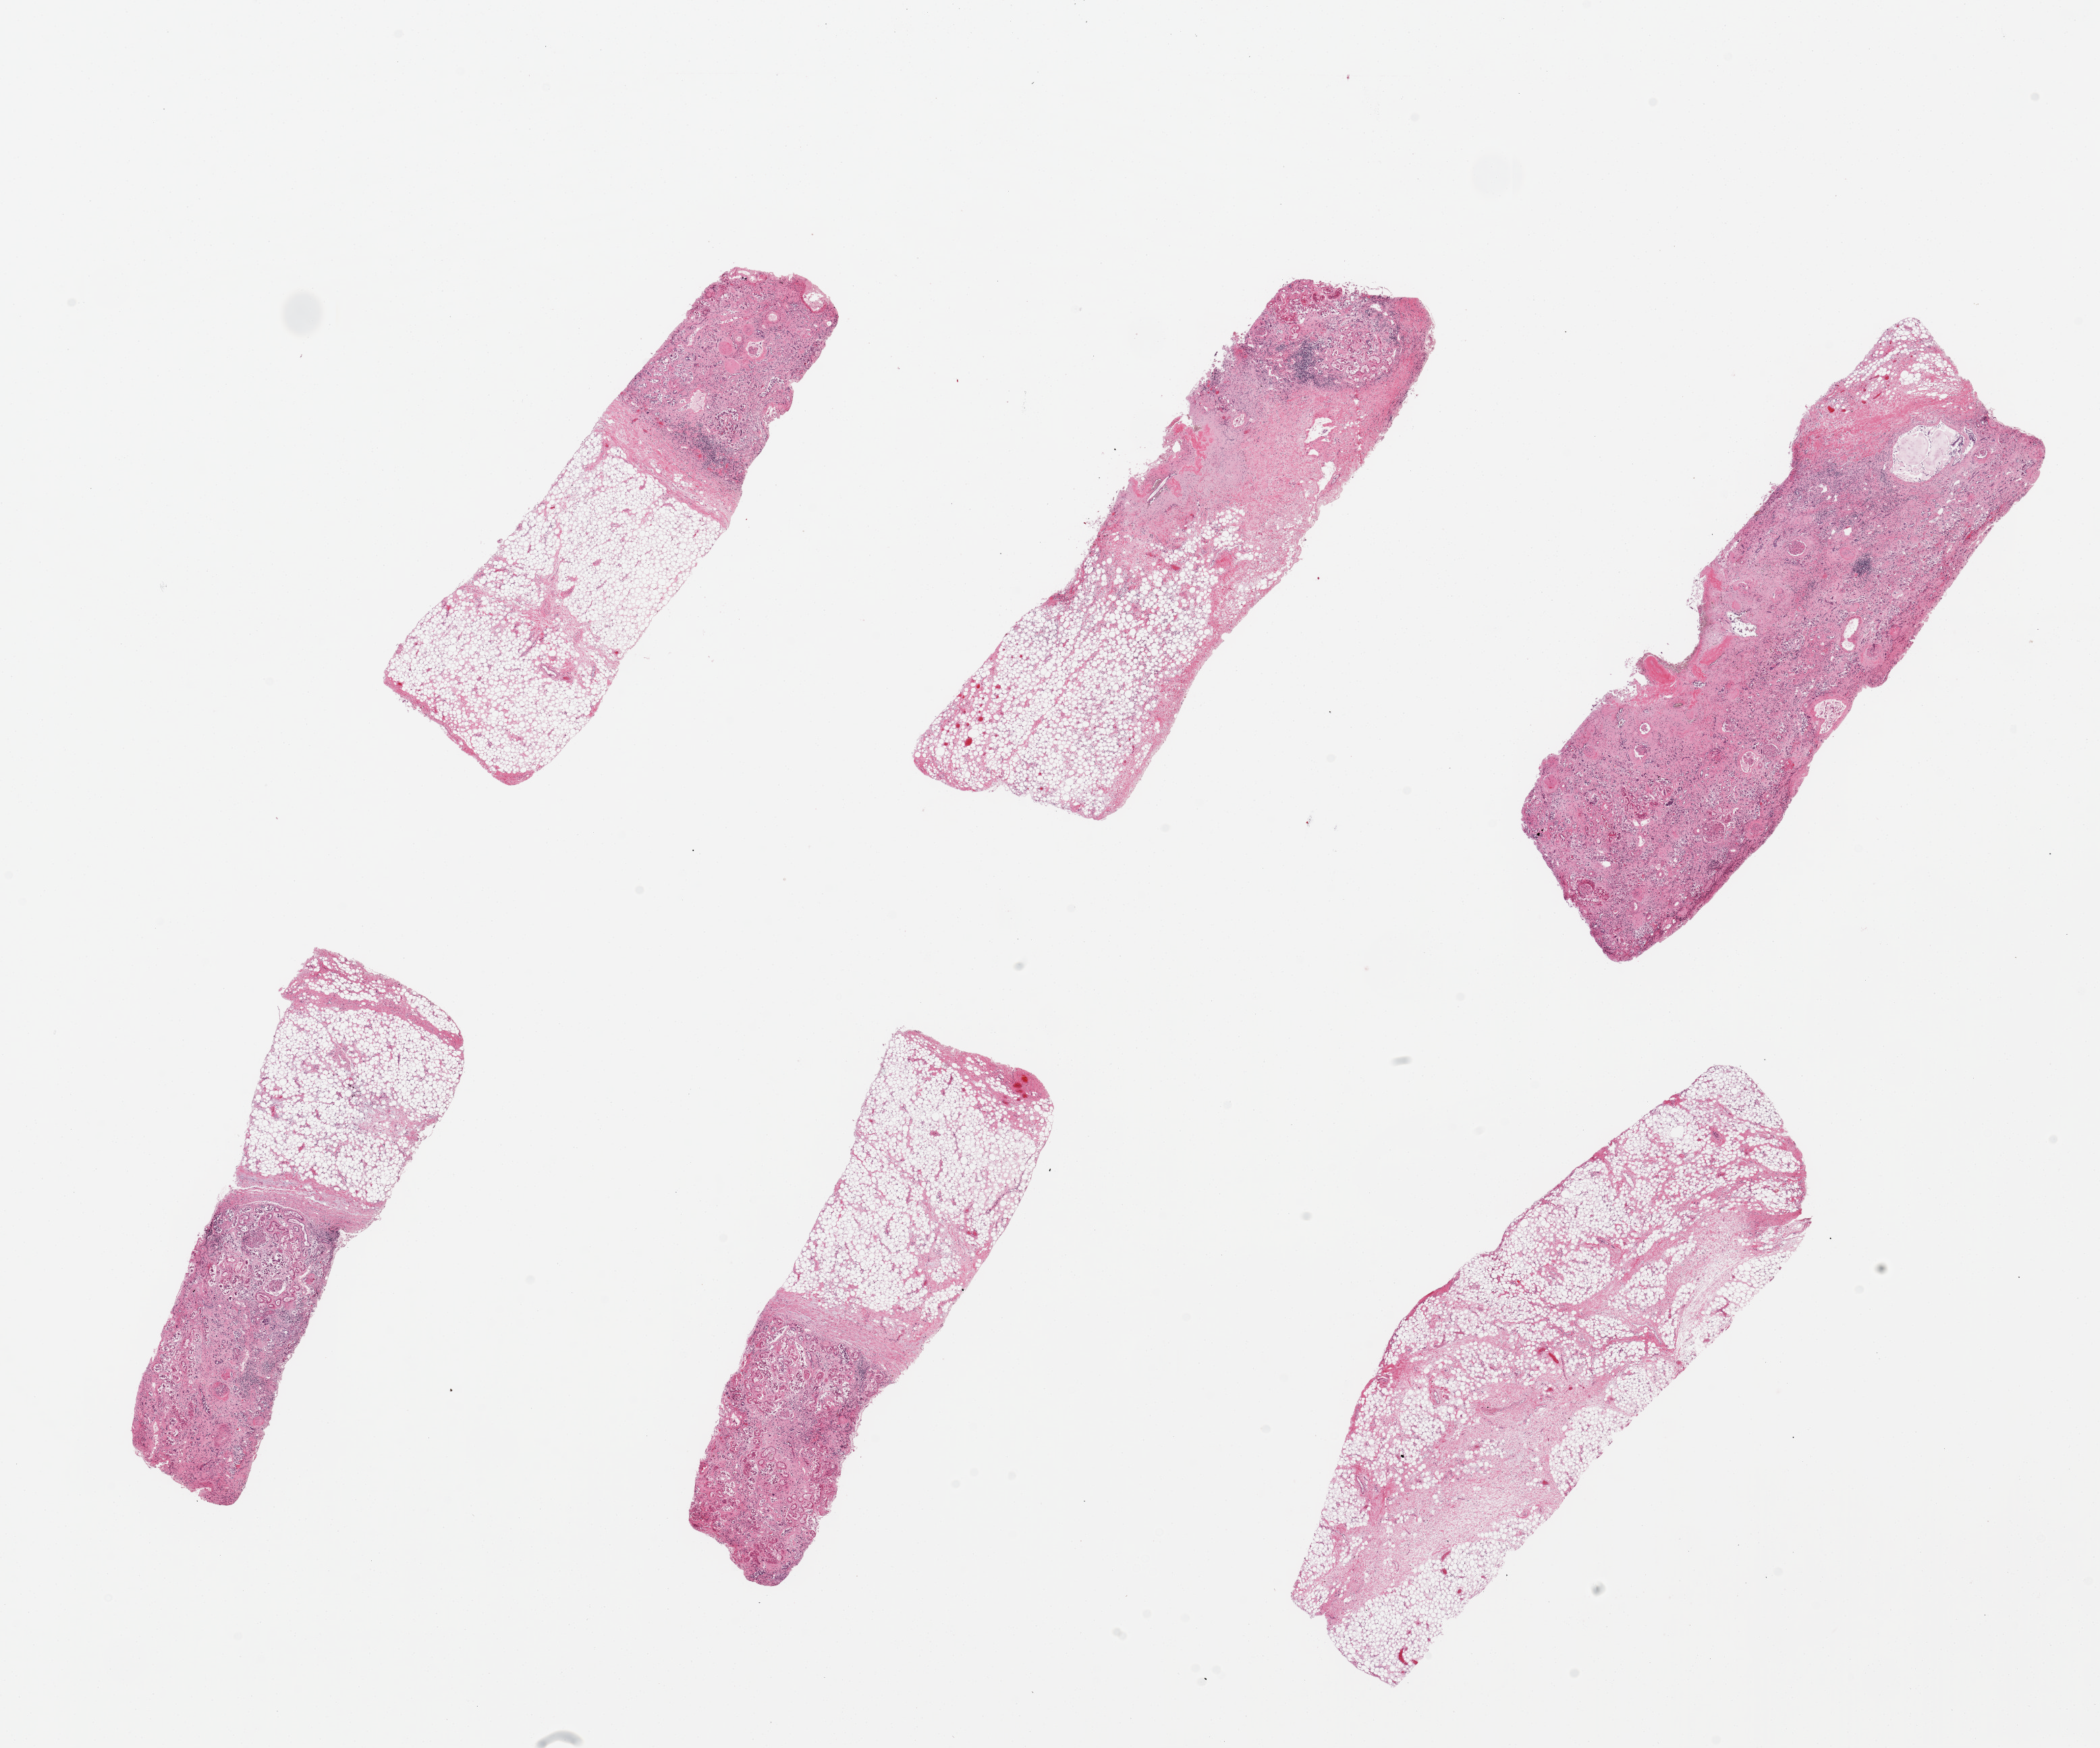
Digitized hematoxylin and eosin (H&E)-stained section — shown as a low-resolution overview of the whole scanned area (about 24.6 x 20.5 mm). Male donor.
Specimen: PAXgene-fixed, paraffin-embedded tissue; target tissue: renal cortex; tissue donor sample.